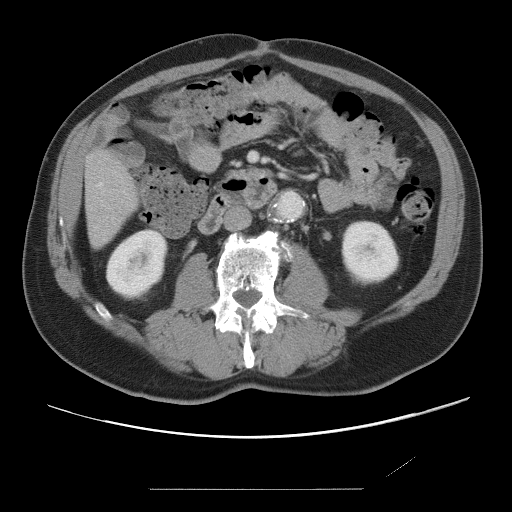
Contrast-enhanced abdominal CT, one axial slice. Slice 15 of 87 in the series (ordered by position). Intravenous contrast given. Soft-tissue window (W 400 / L 40 HU). 5 mm slice thickness. 512 × 512 image matrix. Male patient, age 74 years. Case-level facts recorded for this patient, not image findings: diagnosis: colorectal cancer liver metastases, imaged before liver resection; multiple liver metastases: yes; largest metastasis: 1.1 cm; disease in both lobes: no.
Structures marked on this image (expert manual segmentation):
- hepatic veins: box from (x=99, y=183) to (x=103, y=186) px
- liver: (x=86, y=151)–(x=137, y=248)
- planned liver remnant (the part of the liver to remain after resection): (x=86, y=151)–(x=137, y=248)